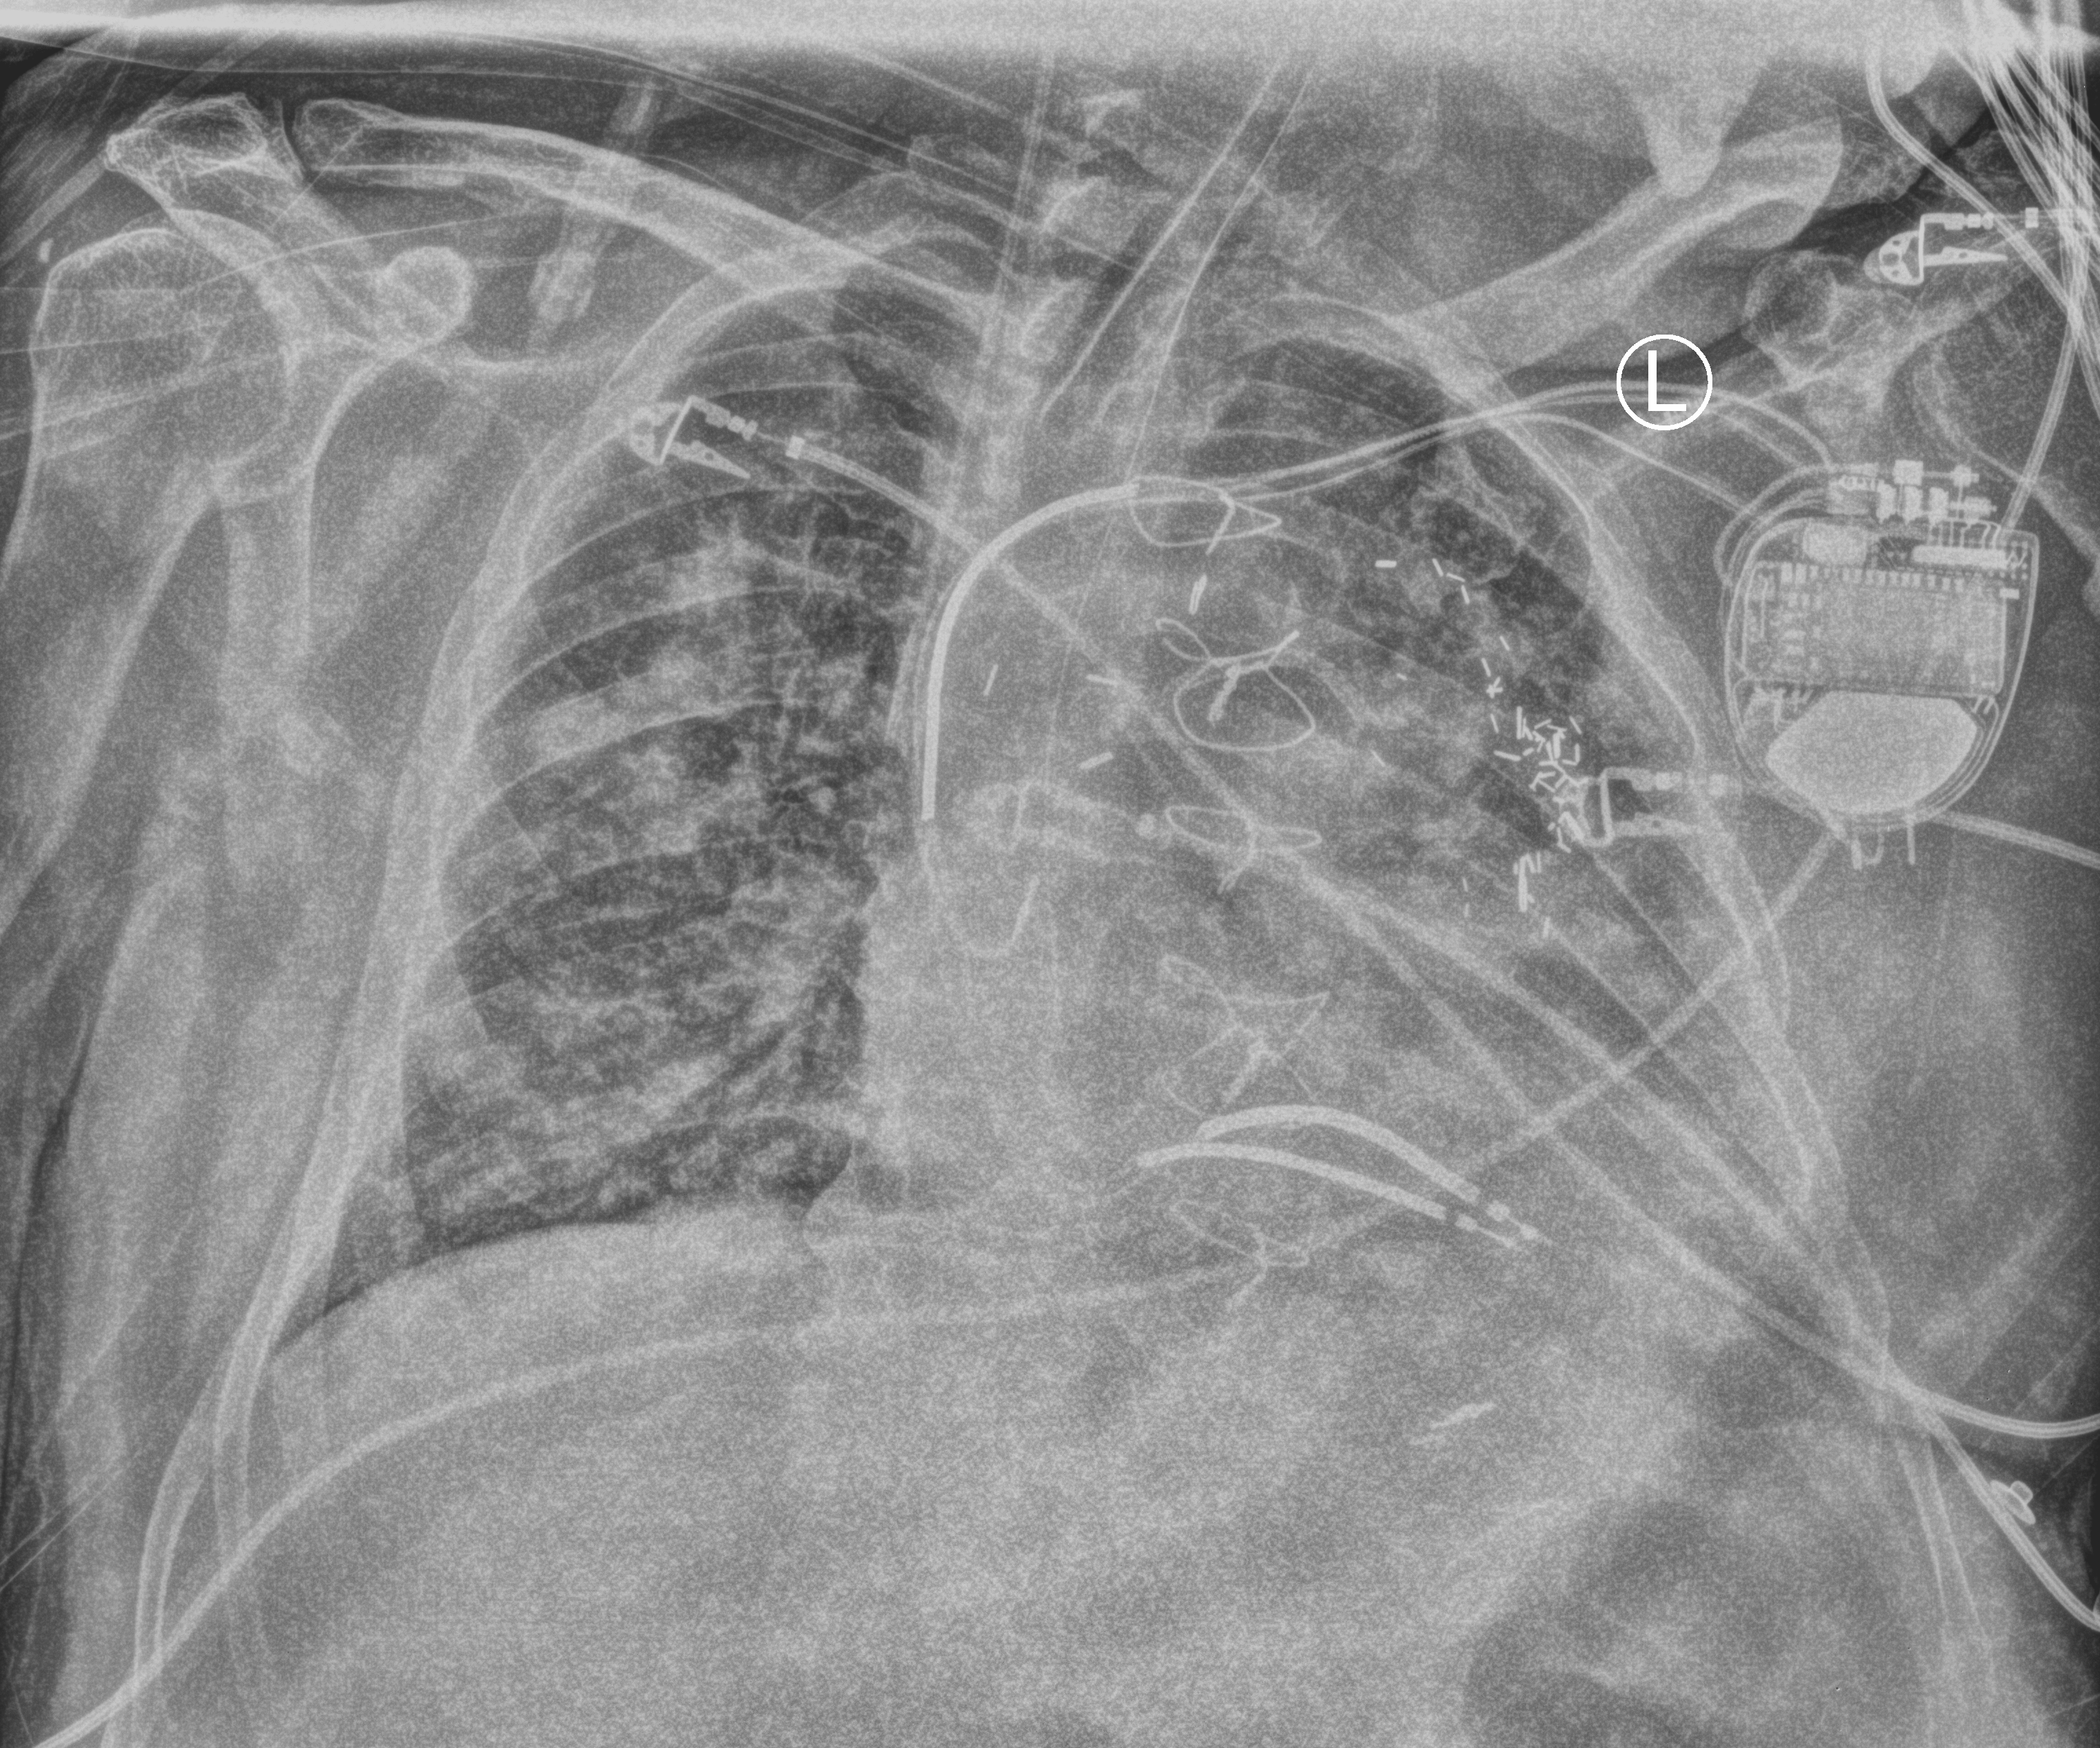
Chest X-ray (portable), anteroposterior (AP) projection. Male patient hospitalised with COVID-19, age 60–74 years.
Hospital-stay facts (about this admission, not read from this image; timing relative to this image not recorded): smoking status (admission record): never; length of hospital stay: 55 days; mechanically ventilated during this hospital stay: yes.